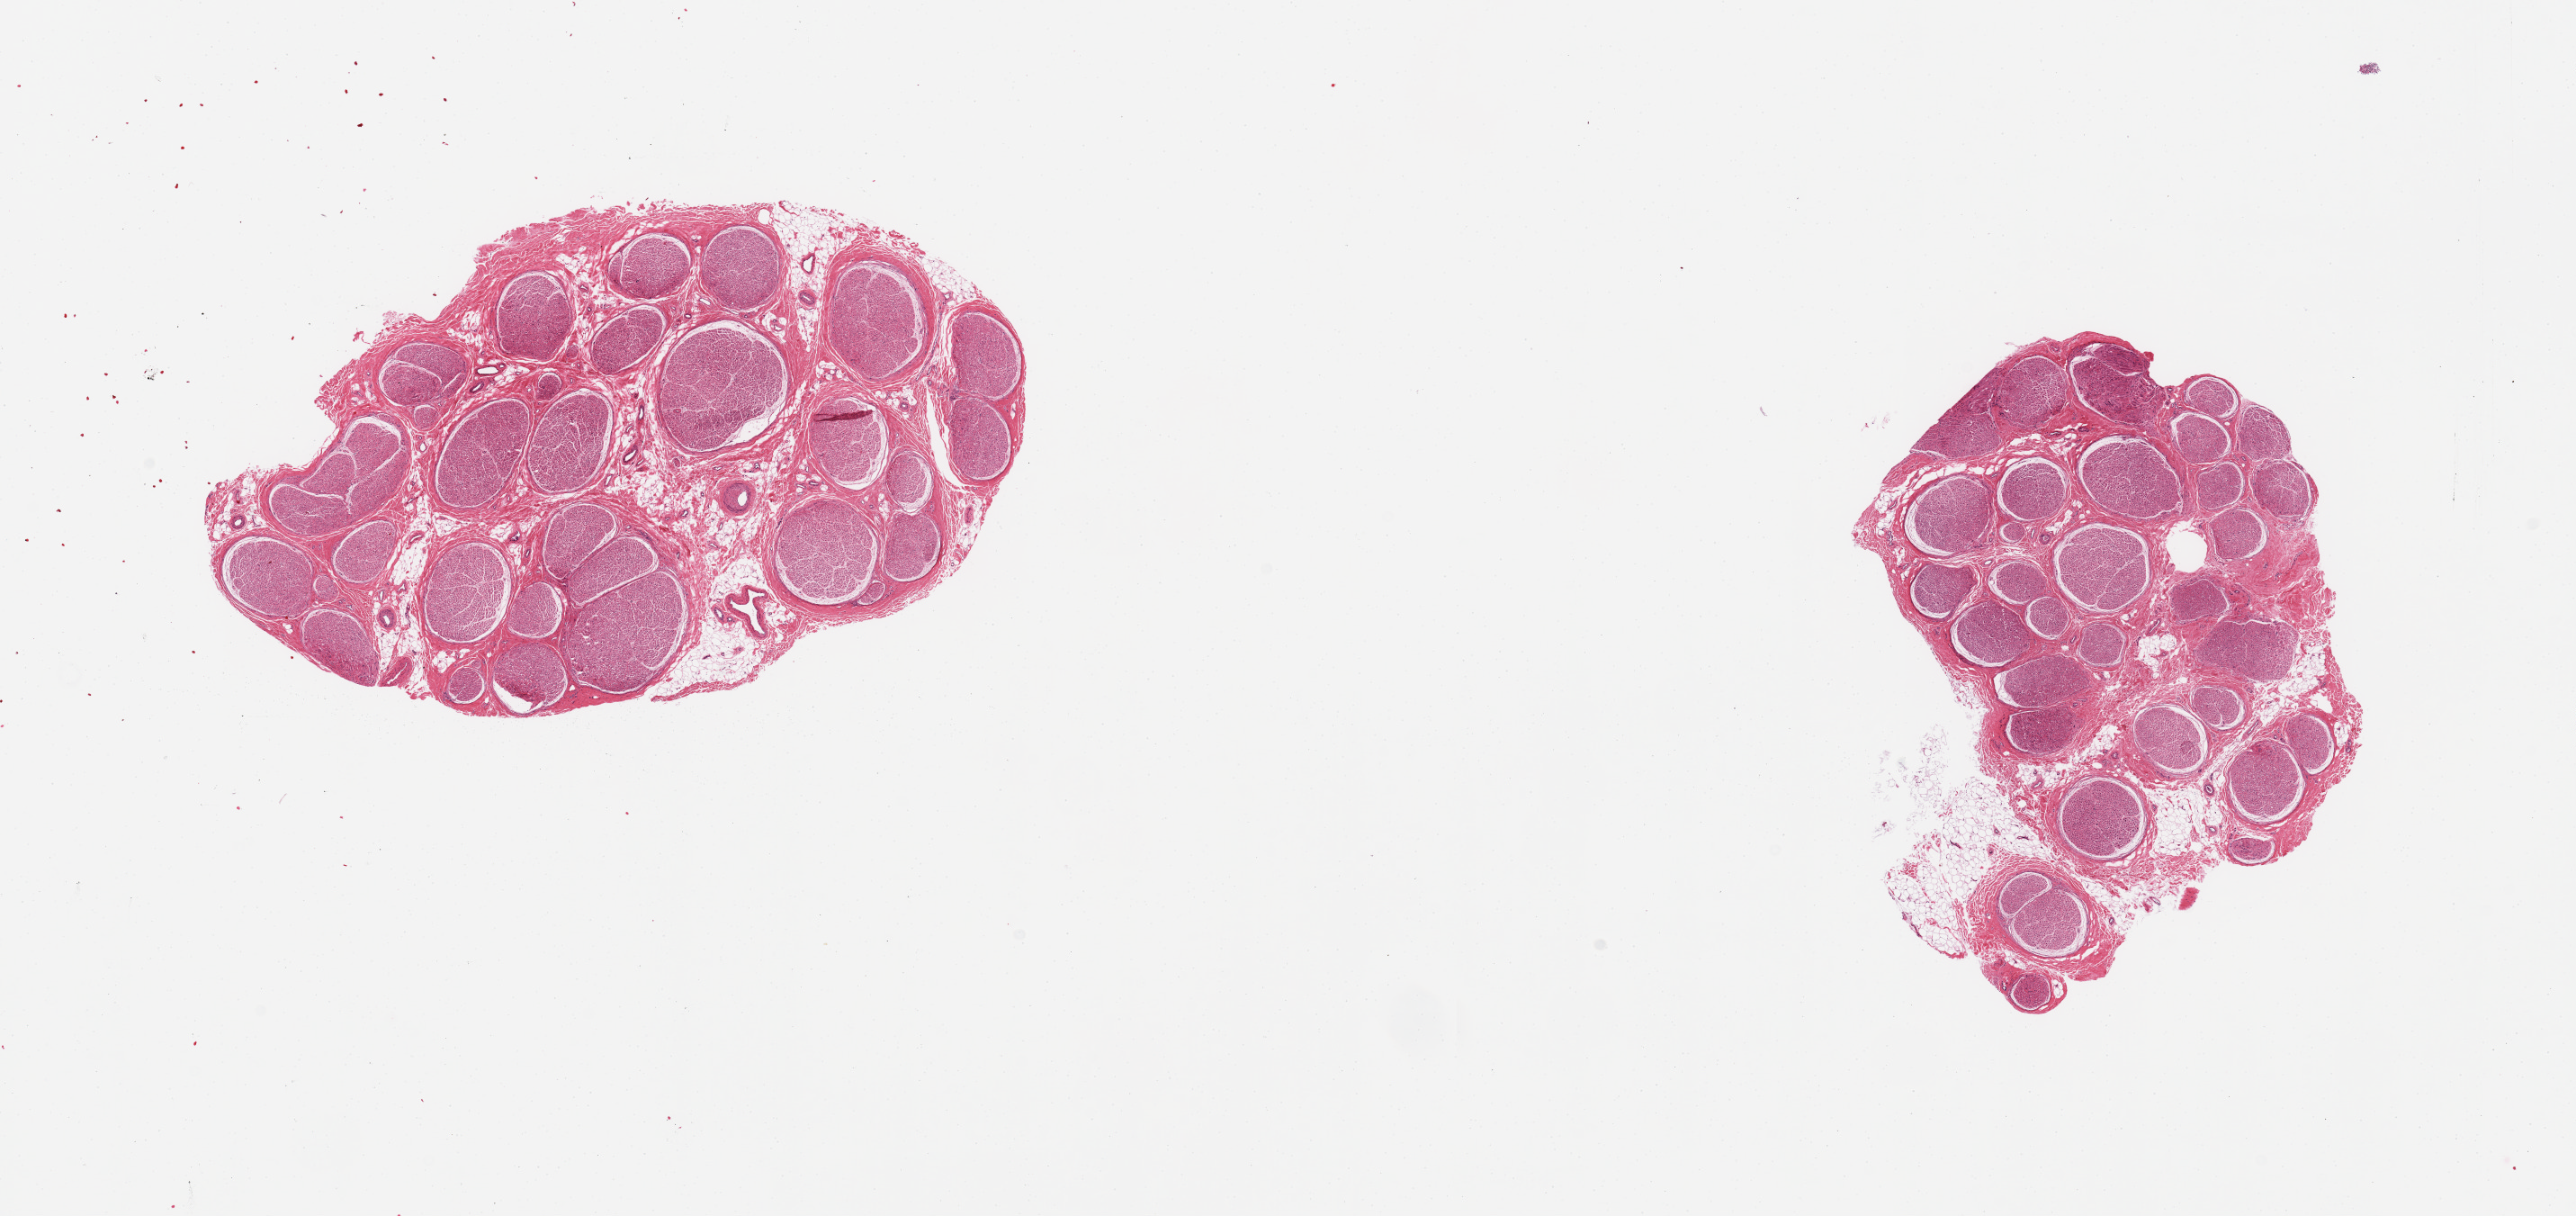
Whole-slide image, haematoxylin and eosin stain, a low-resolution overview of the entire scanned area, about 22.6 x 10.7 mm (acquisition: 20x scan); PAXgene-fixed, paraffin-embedded tissue; target tissue: tibial nerve; tissue donor sample. Donor sex: male.
Review note (as recorded): 2 pieces, includes 5-10% attached and internal fat.